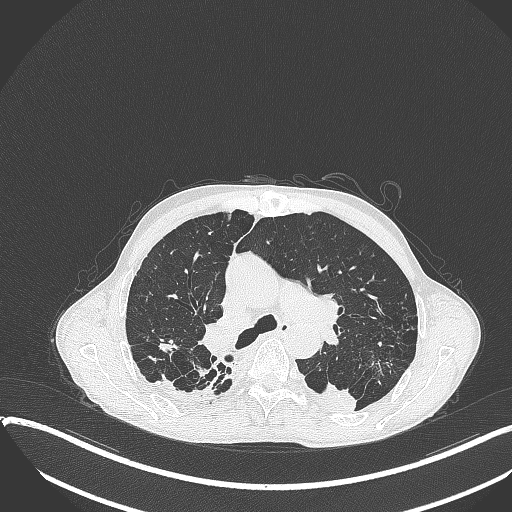
Chest CT, one axial slice; slice 256 of 401 in the series (ordered by position); reconstruction kernel B70f; 120 kVp; lung window (W 1500 / L -600 HU); 1 mm slice thickness; 512 × 512 image matrix, field of view 400 × 400 mm. Patient: male, 57 years. From the clinical record (not read from this slice): clinical TNM (as recorded): T4 N0 M0.
Structures marked on this image (rectangle marked by the reading radiologist):
- lung tumour (recorded histology: squamous cell carcinoma): bounding box [x1, y1, x2, y2] px = [305, 377, 362, 421]